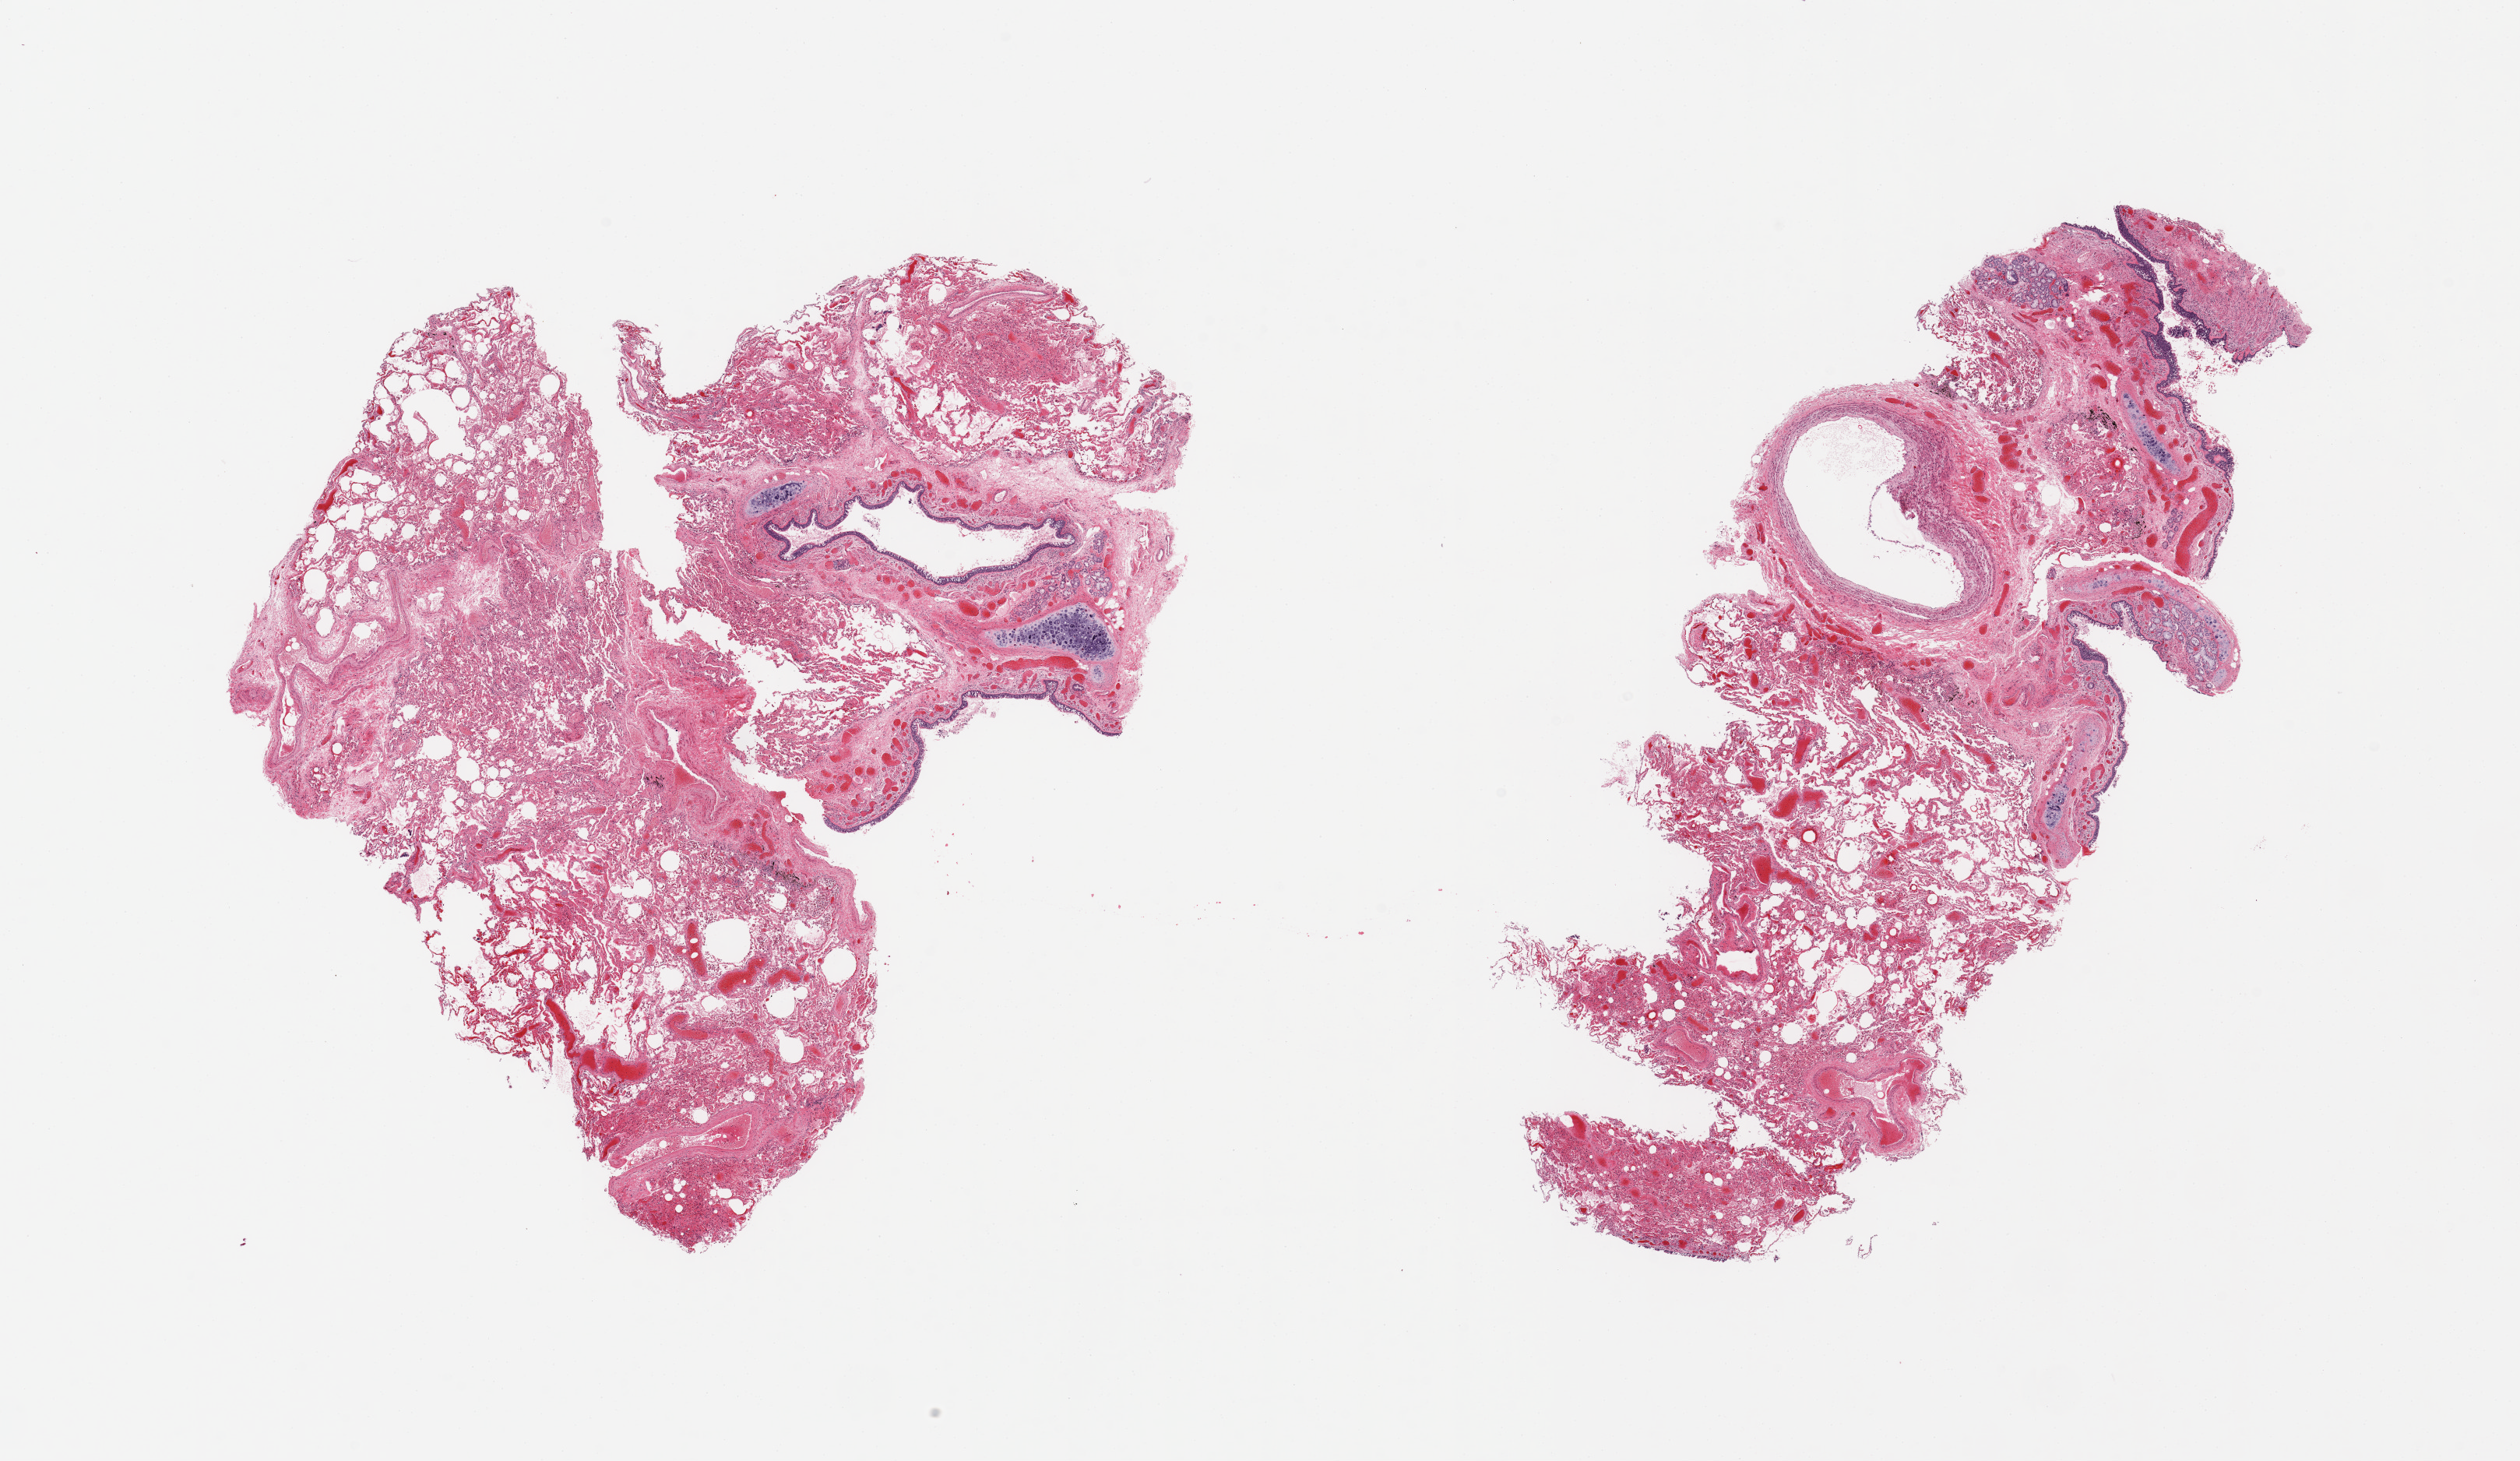
Haematoxylin and eosin whole-slide image — low-resolution overview of the scanned area, about 25.6 x 14.8 mm, PAXgene-fixed, paraffin-embedded tissue, sampled site (target tissue): lung, tissue donor sample. Donor: male.
Review note (as recorded): 2 pieces, mild congestion, well-preserved bronchial mucosa.